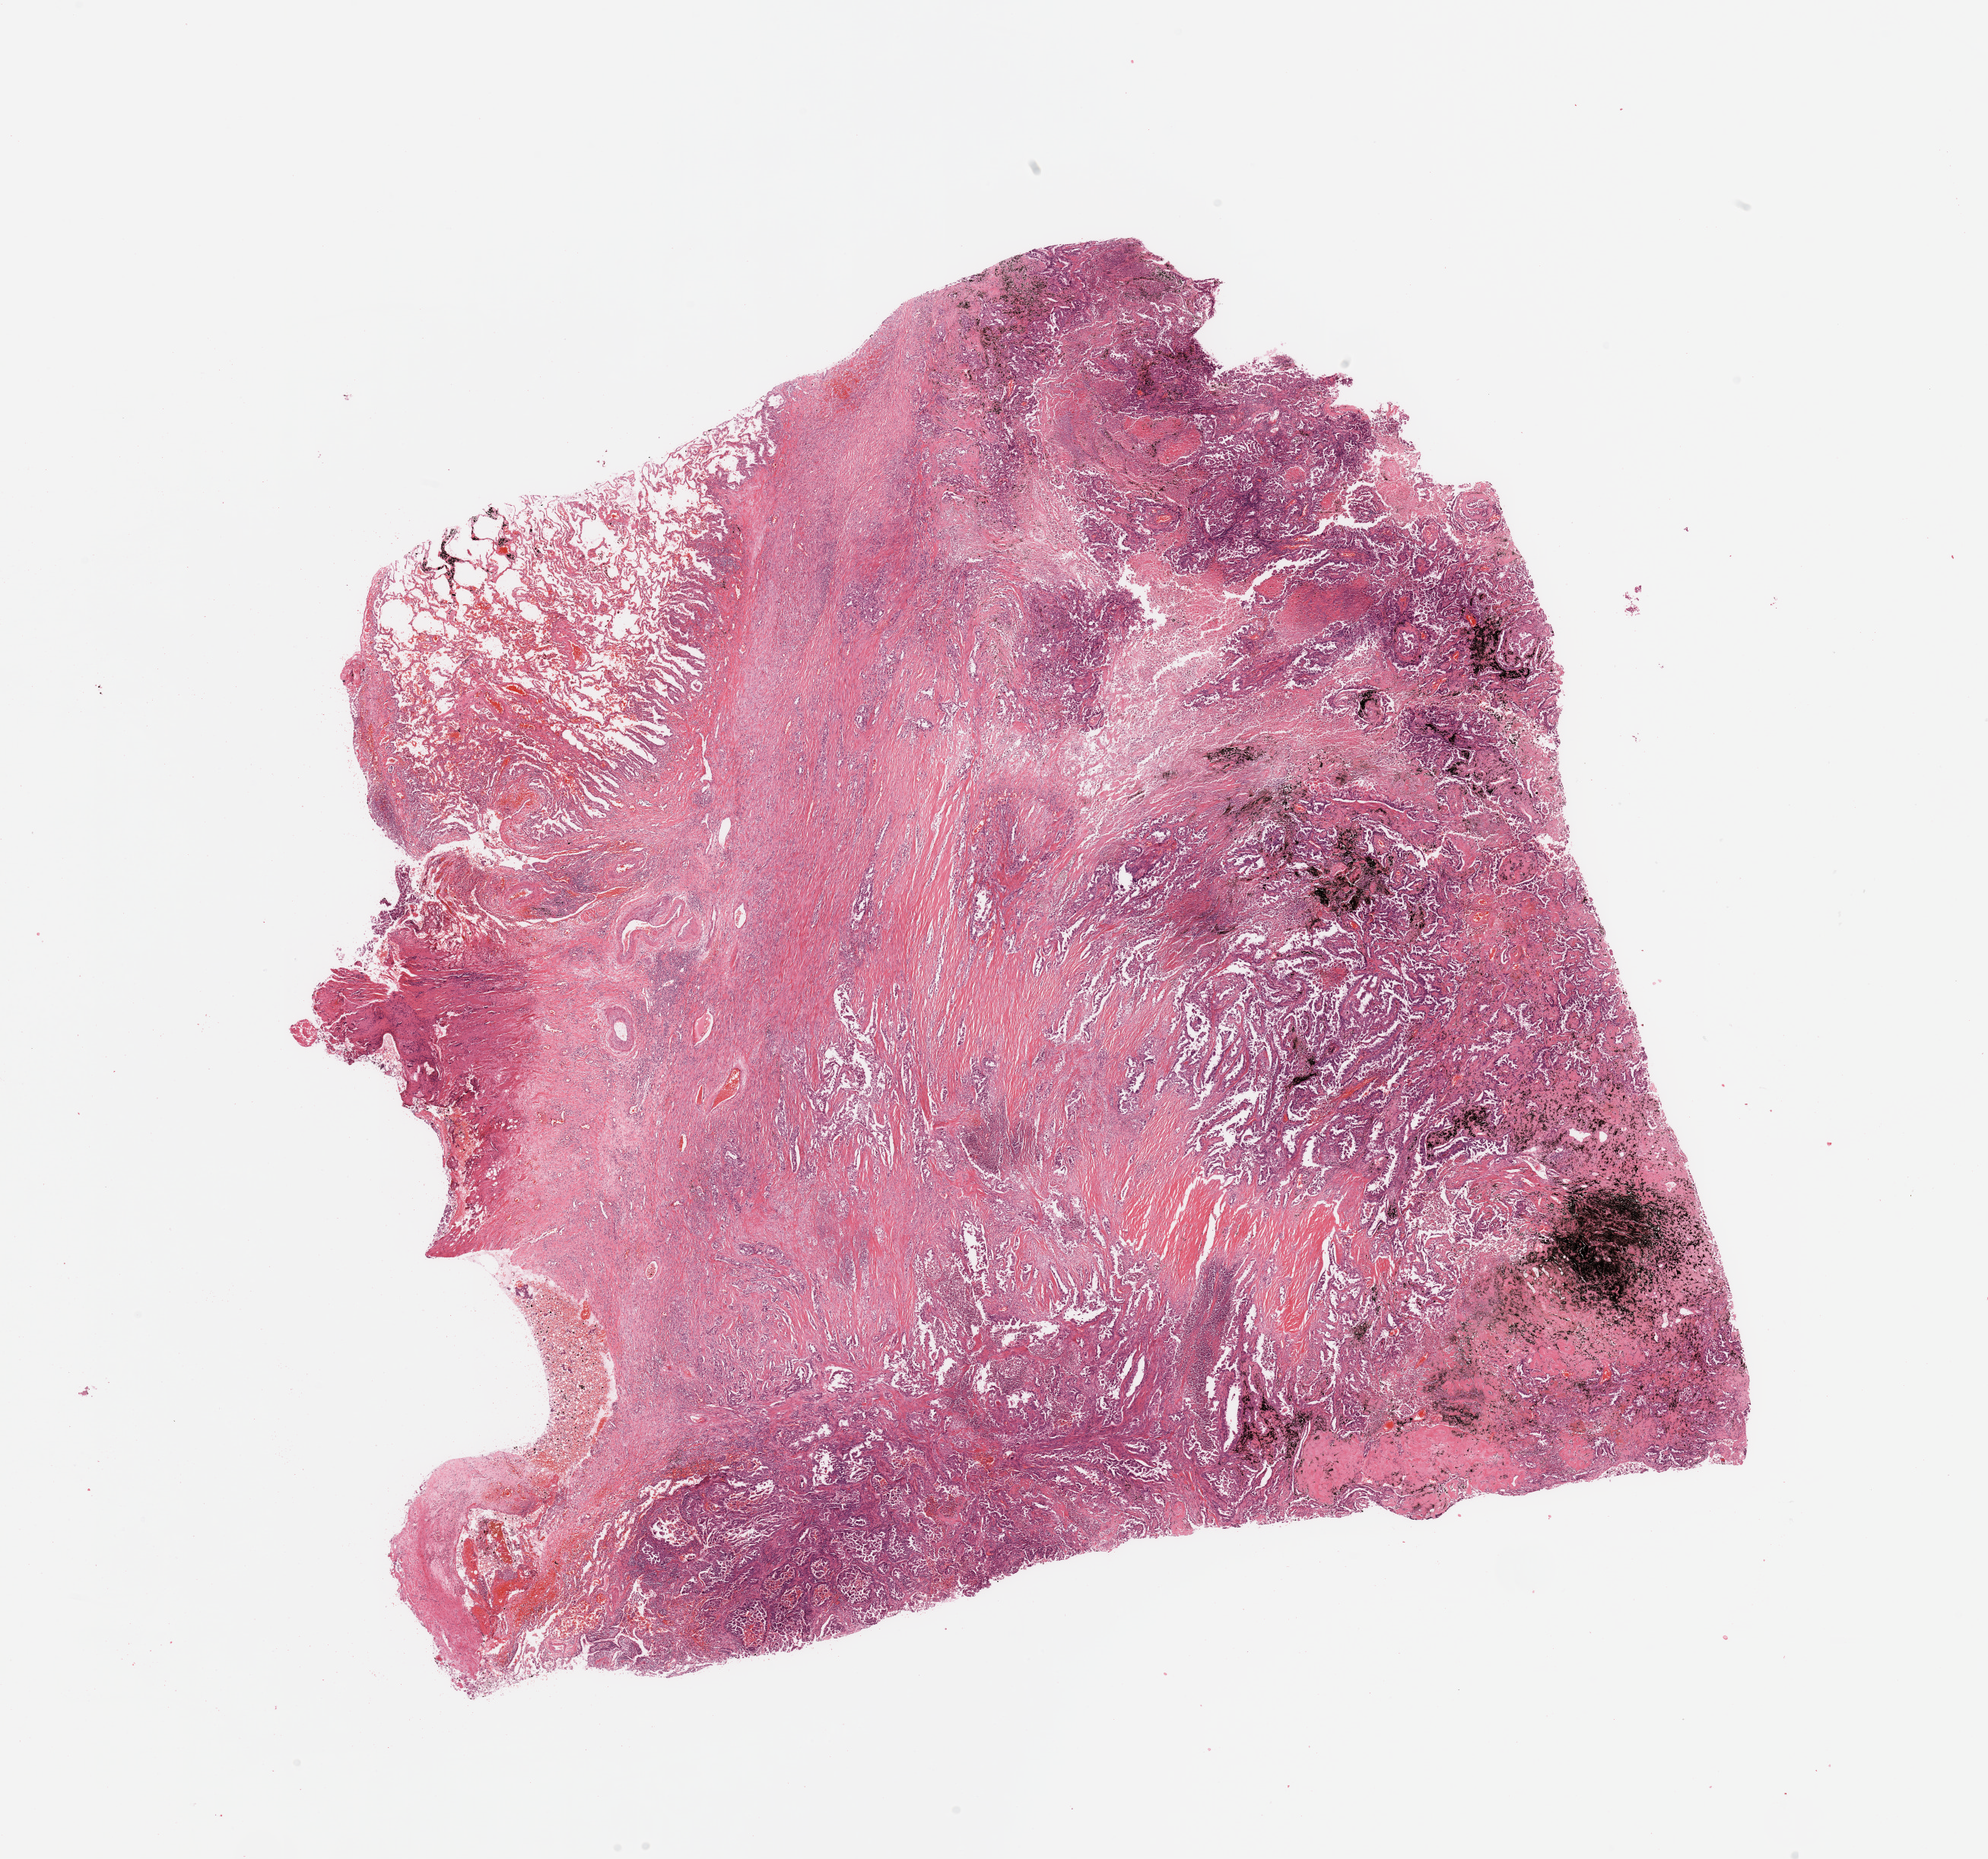
Digitized H&E tissue section (whole slide), a low-resolution overview of the entire scanned area, about 20.7 x 19.3 mm (slide scanned at 20x). Lung, tumour tissue. Male, 56 y/o. Histologic grade: G2 (moderately differentiated).
* diagnosis: Adenocarcinoma, NOS
* AJCC pathologic stage: IB